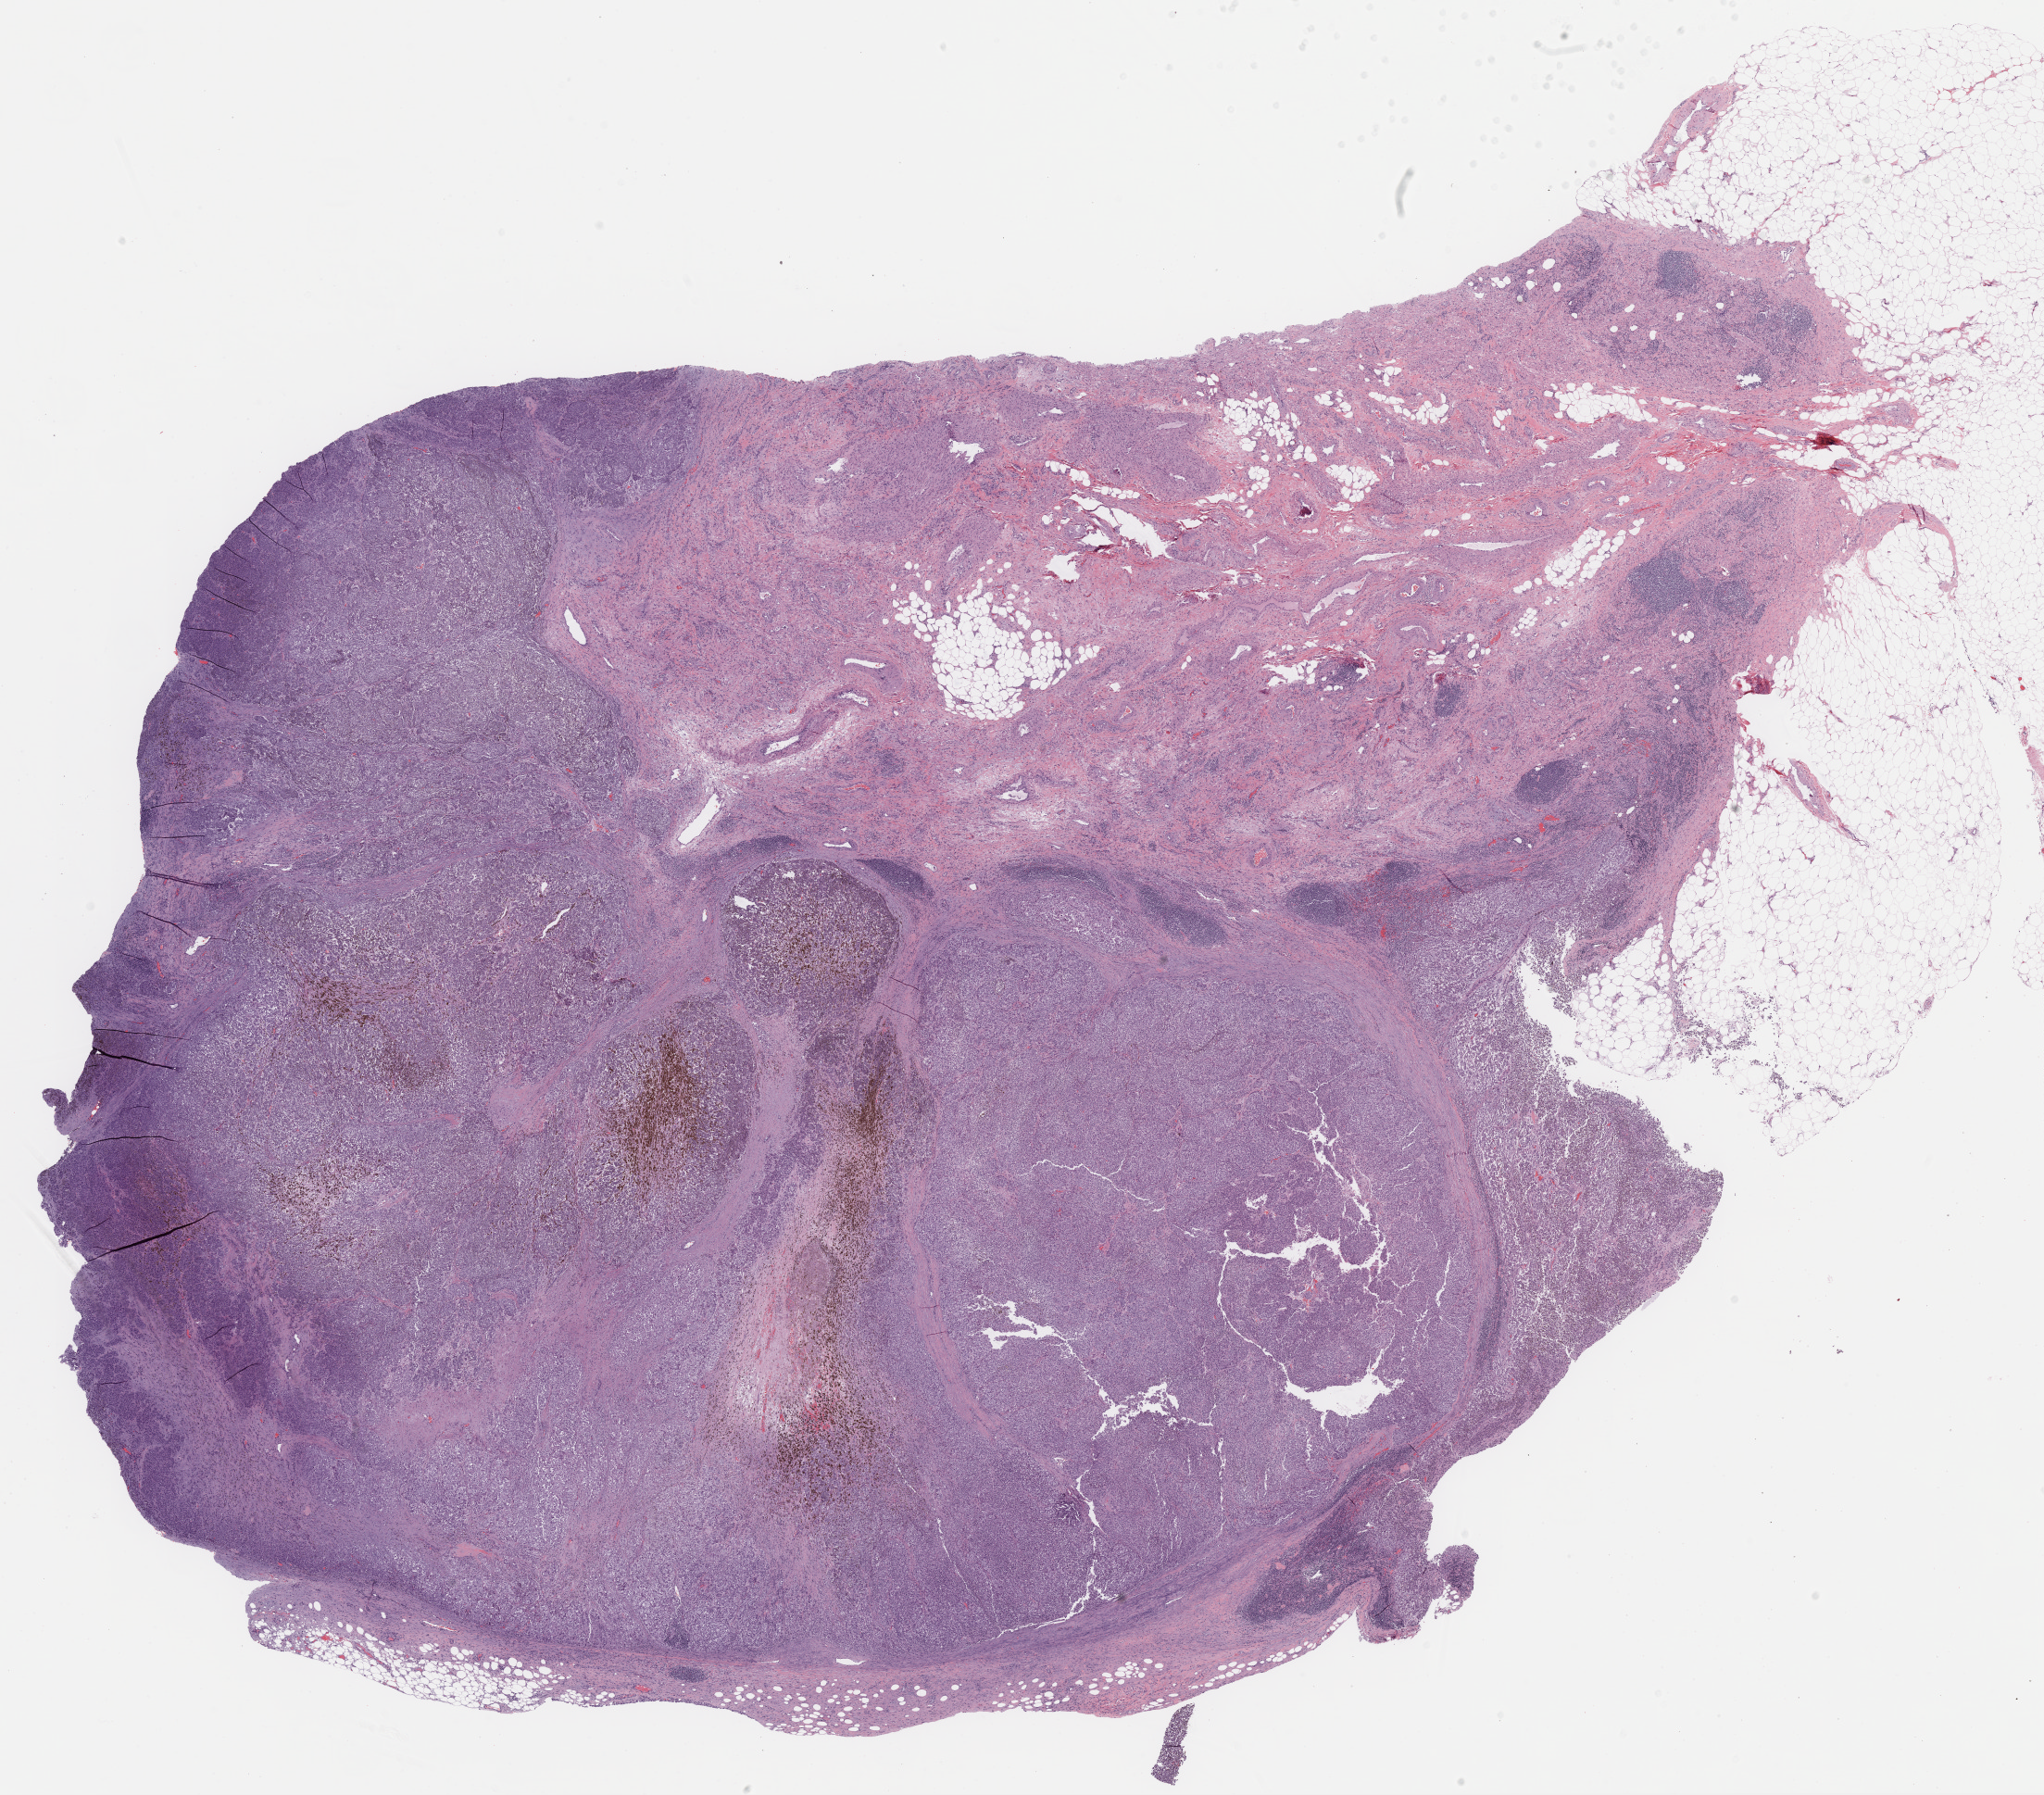
Whole-slide histology image, H&E — low-resolution overview of the scanned area, about 17.8 x 15.6 mm; FFPE section; metastatic tumour sample. Male patient; age at initial diagnosis 58 years.
* this section: metastatic tumour tissue
* patient diagnosis: Malignant melanoma, NOS